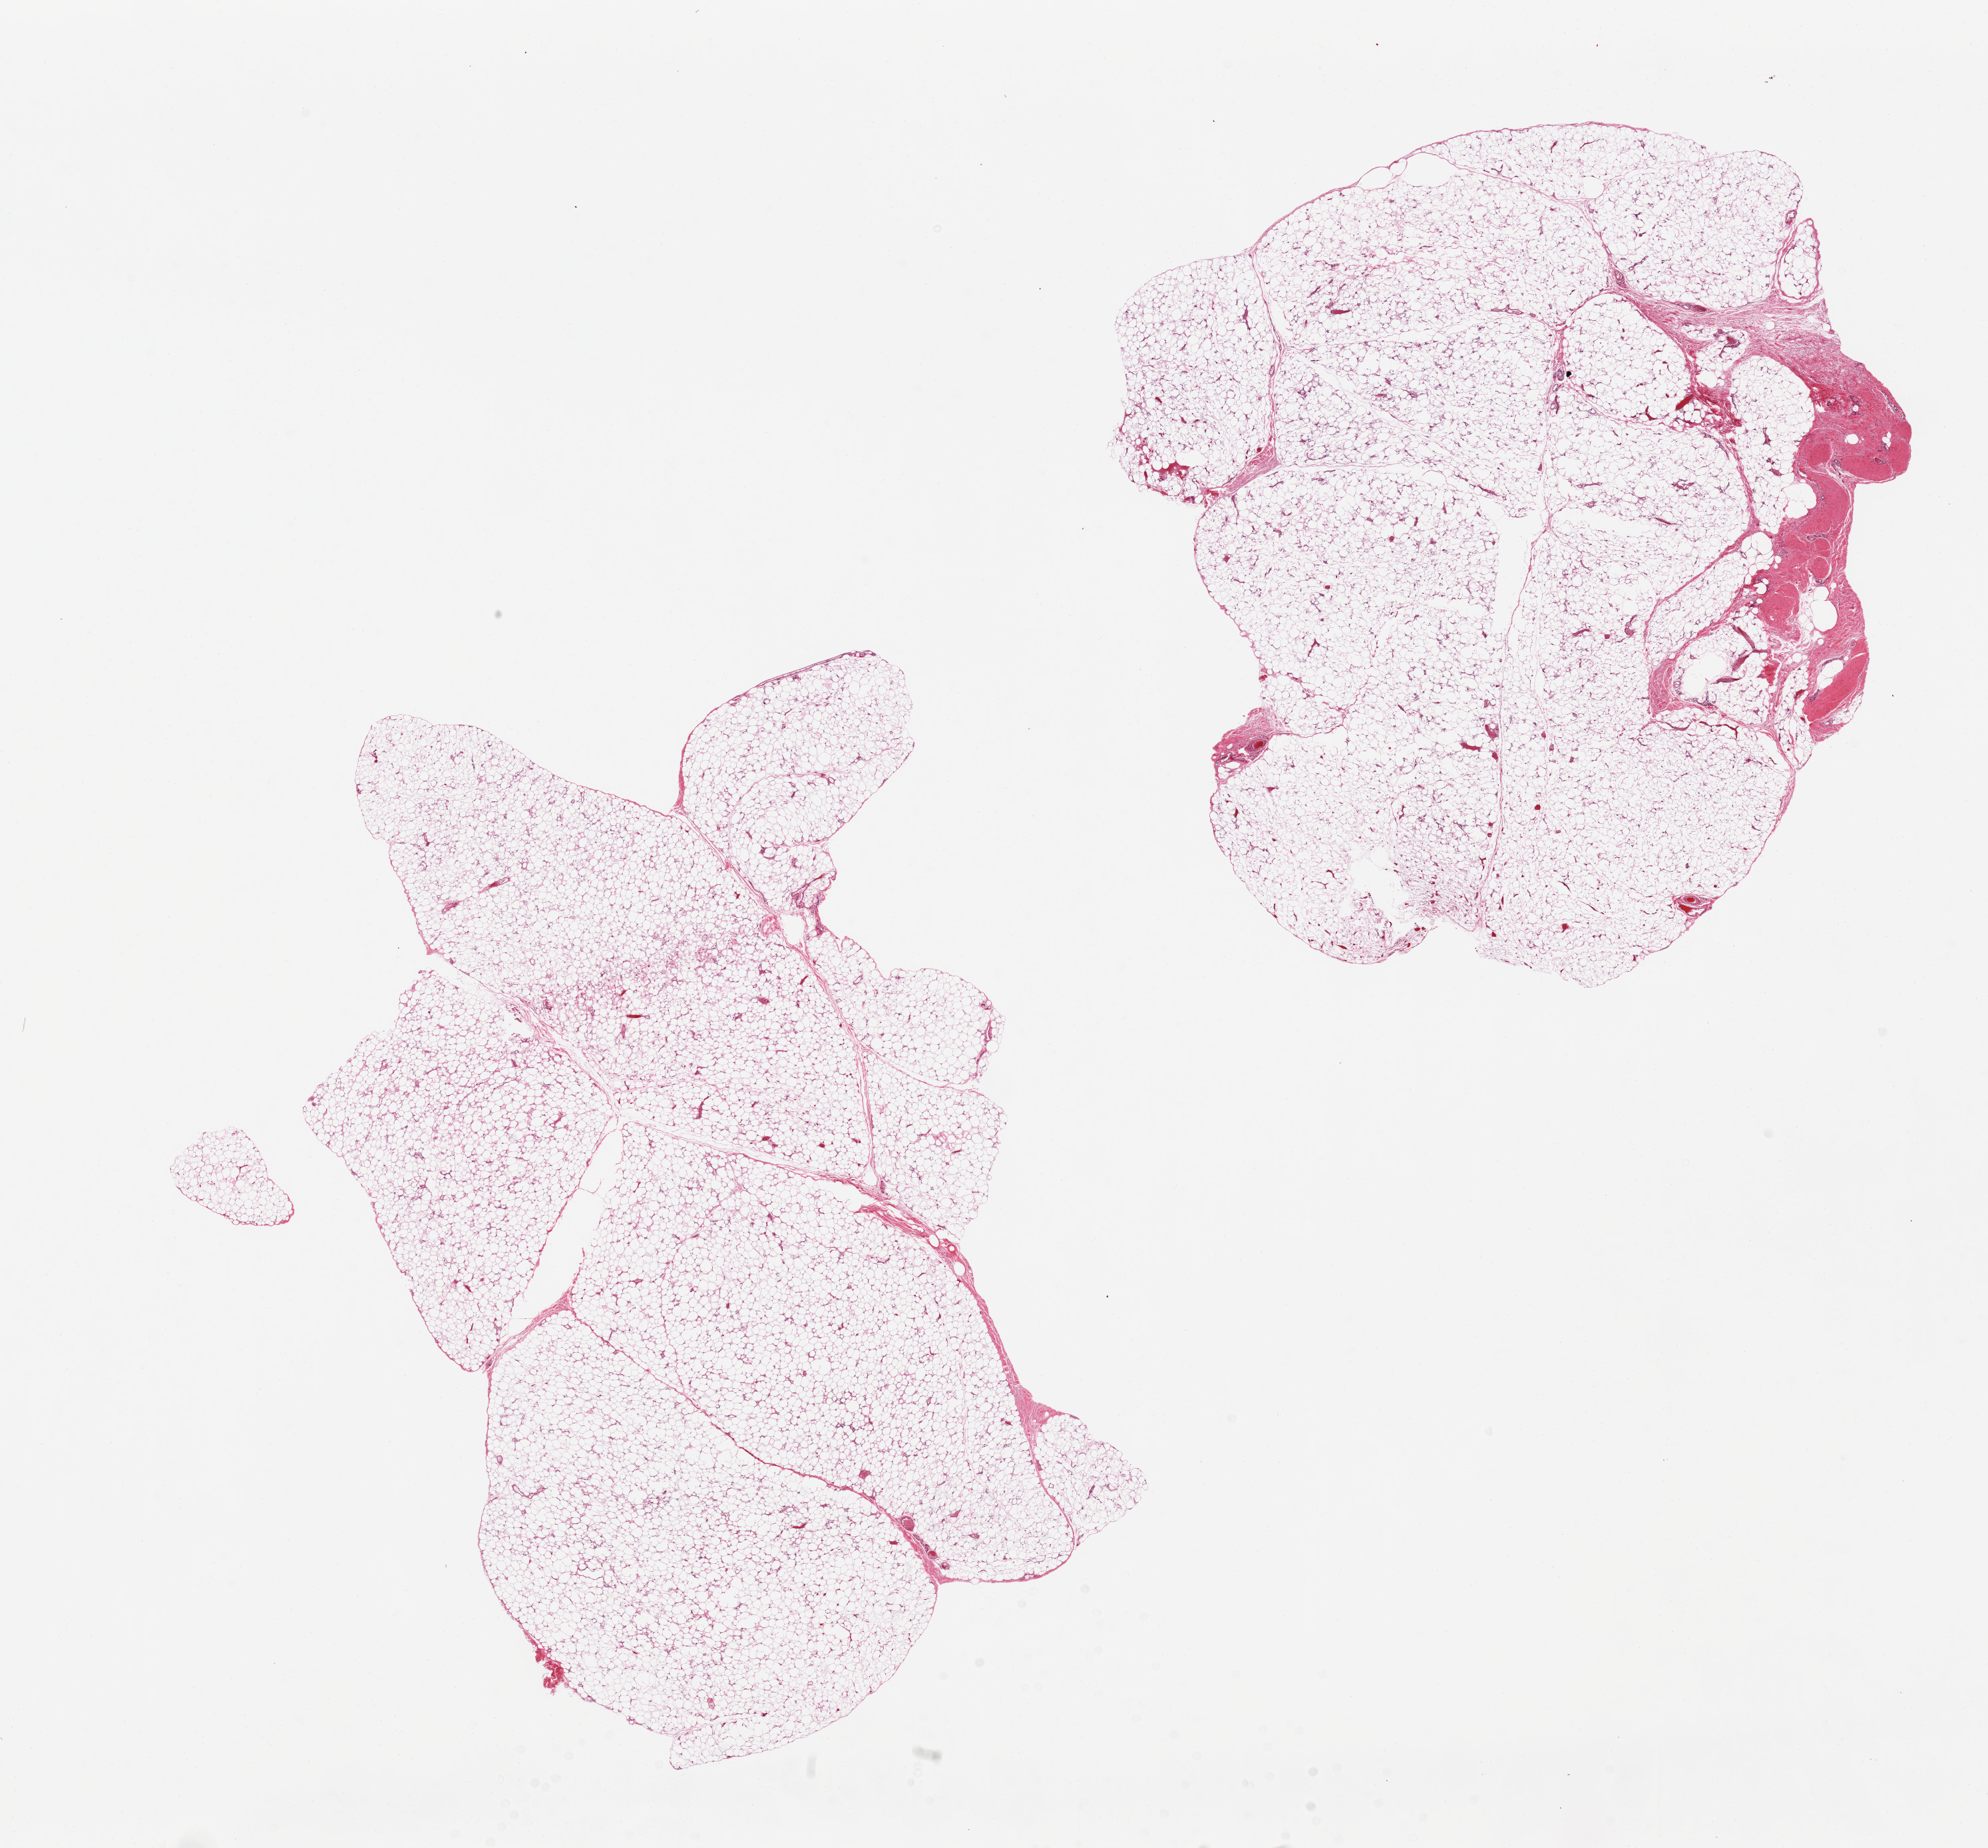
Whole-slide image, hematoxylin and eosin (H&E) stain, brightfield — whole scanned area (about 23.6 x 22.0 mm, acquisition: 20x scan) shown as a low-resolution overview, PAXgene-fixed paraffin-embedded (PFPE) section, target tissue: adipose tissue, donor tissue sample. Donor: male.
Review note (as recorded): 2 pieces, ~10% fascia/connective tissue.